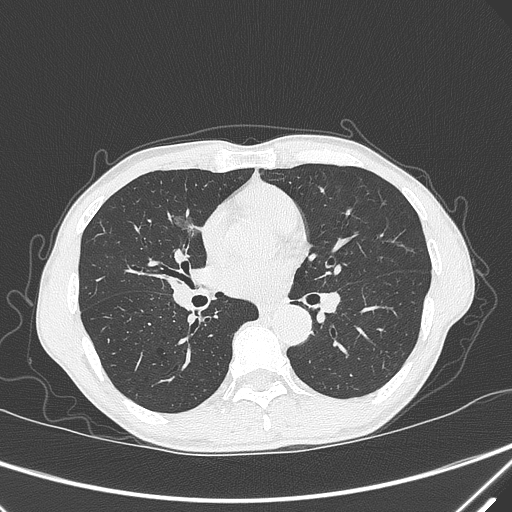
Chest CT, one axial slice. Lung window (W 1500 / L -600 HU). 512 × 512 image matrix. Patient: male, 67 years. From the clinical record (not read from this slice): clinical TNM (as recorded): T1c N0 M0.
Outlined on this slice (bounding box drawn by a radiologist):
- lung tumour (recorded histology: adenocarcinoma): box from (x=169, y=206) to (x=200, y=242) px